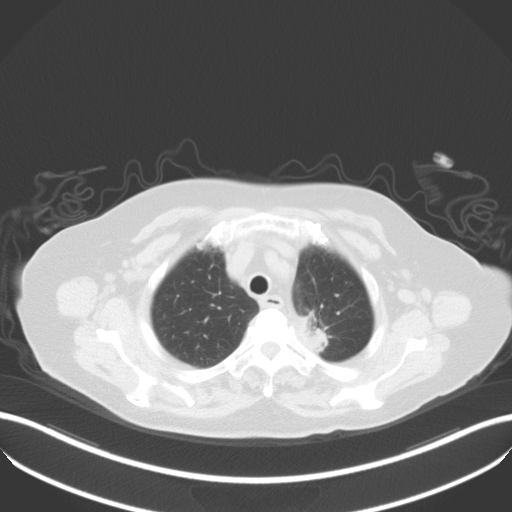
Chest CT, one axial slice; slice 40 of 50 in the series (ordered by position); reconstruction kernel B31f; 100 kVp; lung window (W 1500 / L -600 HU); 5 mm slice thickness; 512 × 512 image matrix, field of view 400 × 400 mm. Female patient, age 81 years. Case-level facts recorded for this patient, not image findings: clinical TNM (as recorded): T2a N0 M0.
Outlined on this slice (rectangle marked by the reading radiologist):
- lung tumour (recorded histology: adenocarcinoma): bounding box <291,305,335,369> (left, top, right, bottom; pixels)